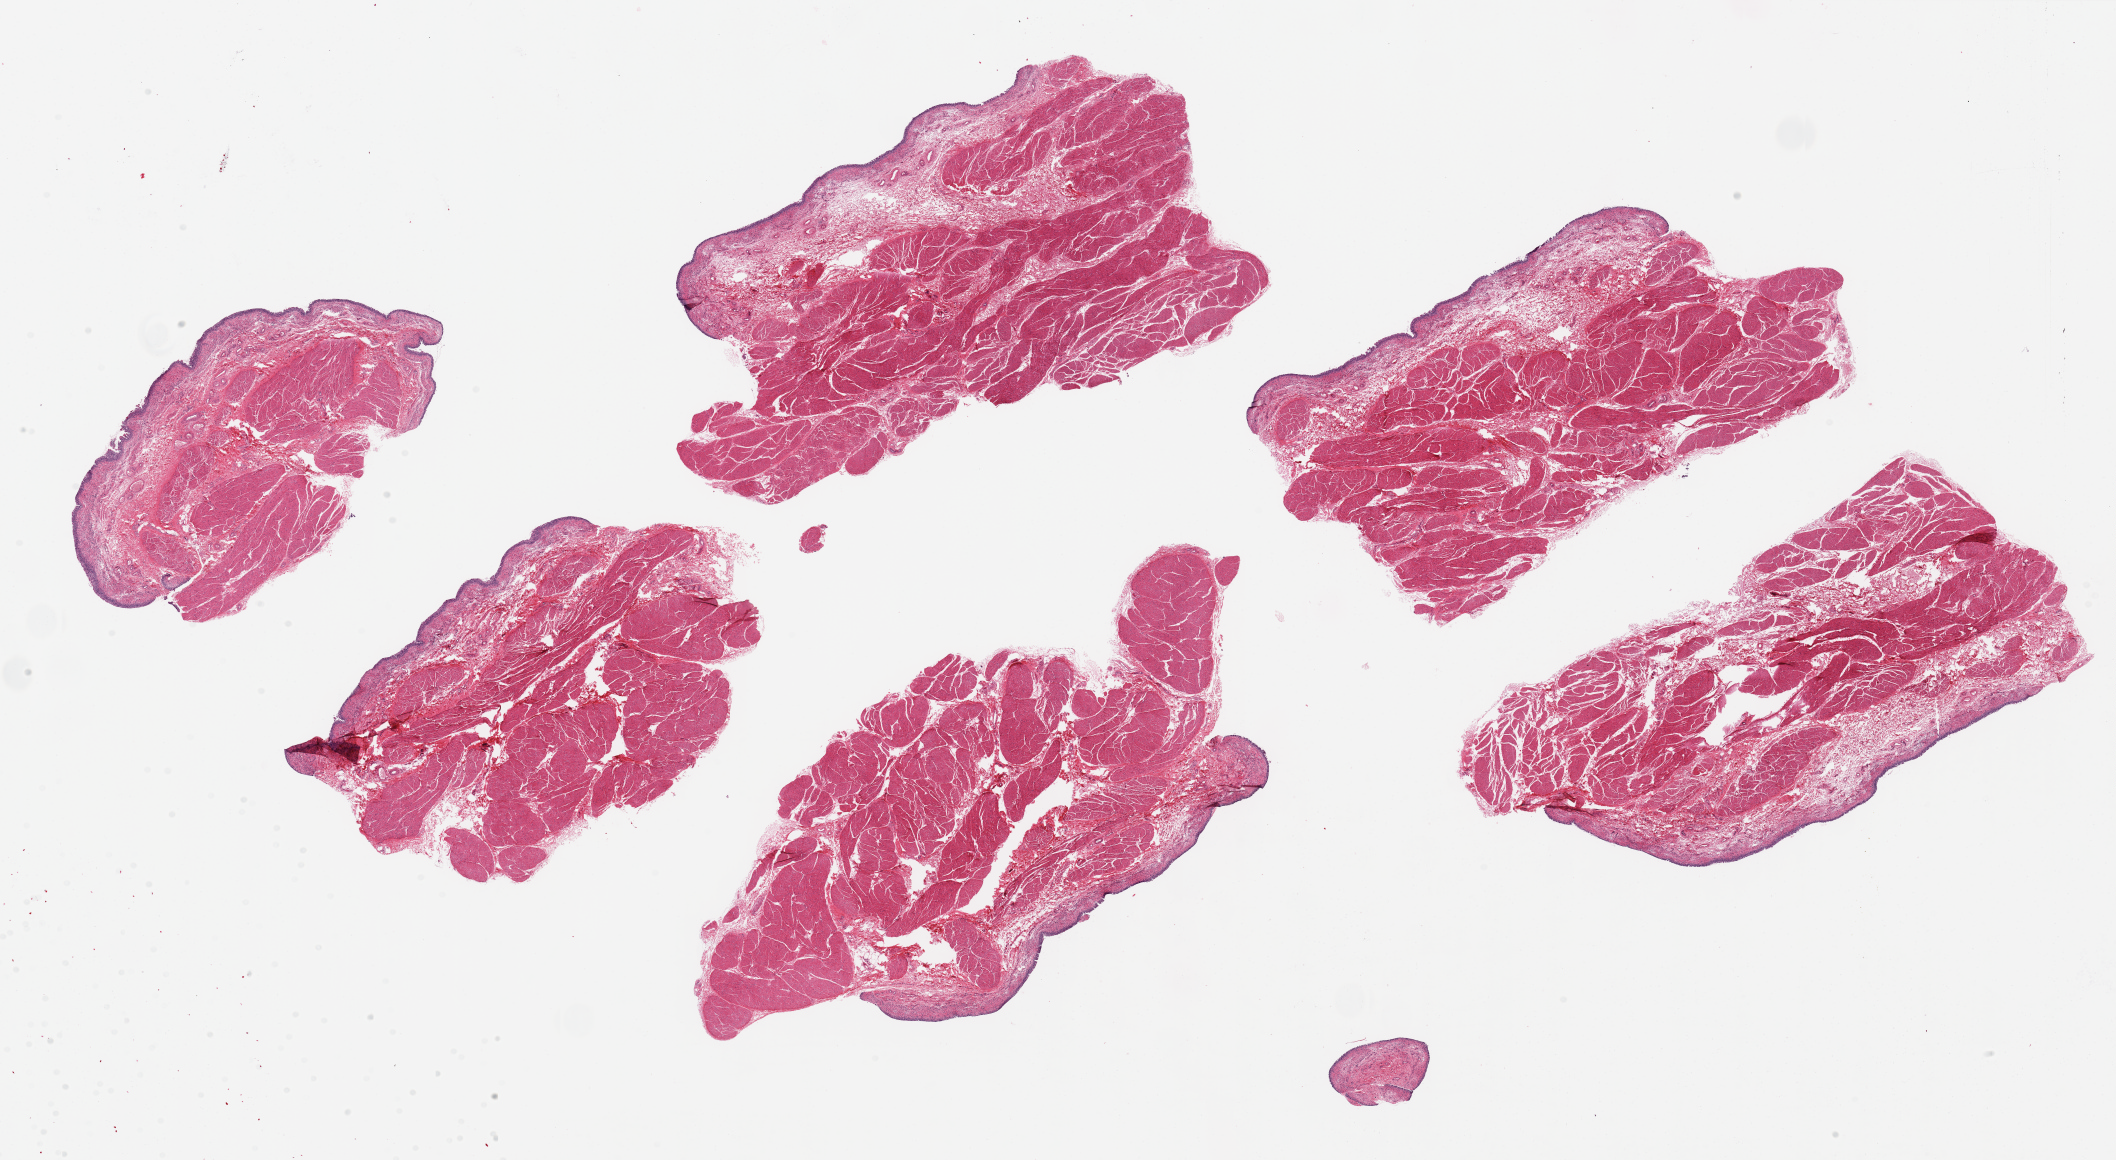
Hematoxylin and eosin (H&E) whole-slide image, low-resolution overview of the scanned area, about 33.5 x 18.3 mm (acquisition: 20x scan); PAXgene-fixed paraffin-embedded (PFPE) section; section of urinary bladder (target tissue); donor tissue sample. Donor sex: female.
Reviewer comment on this tissue sample: 4 pieces, up 8x4.5 mm; extensive patchy surface sloughing.